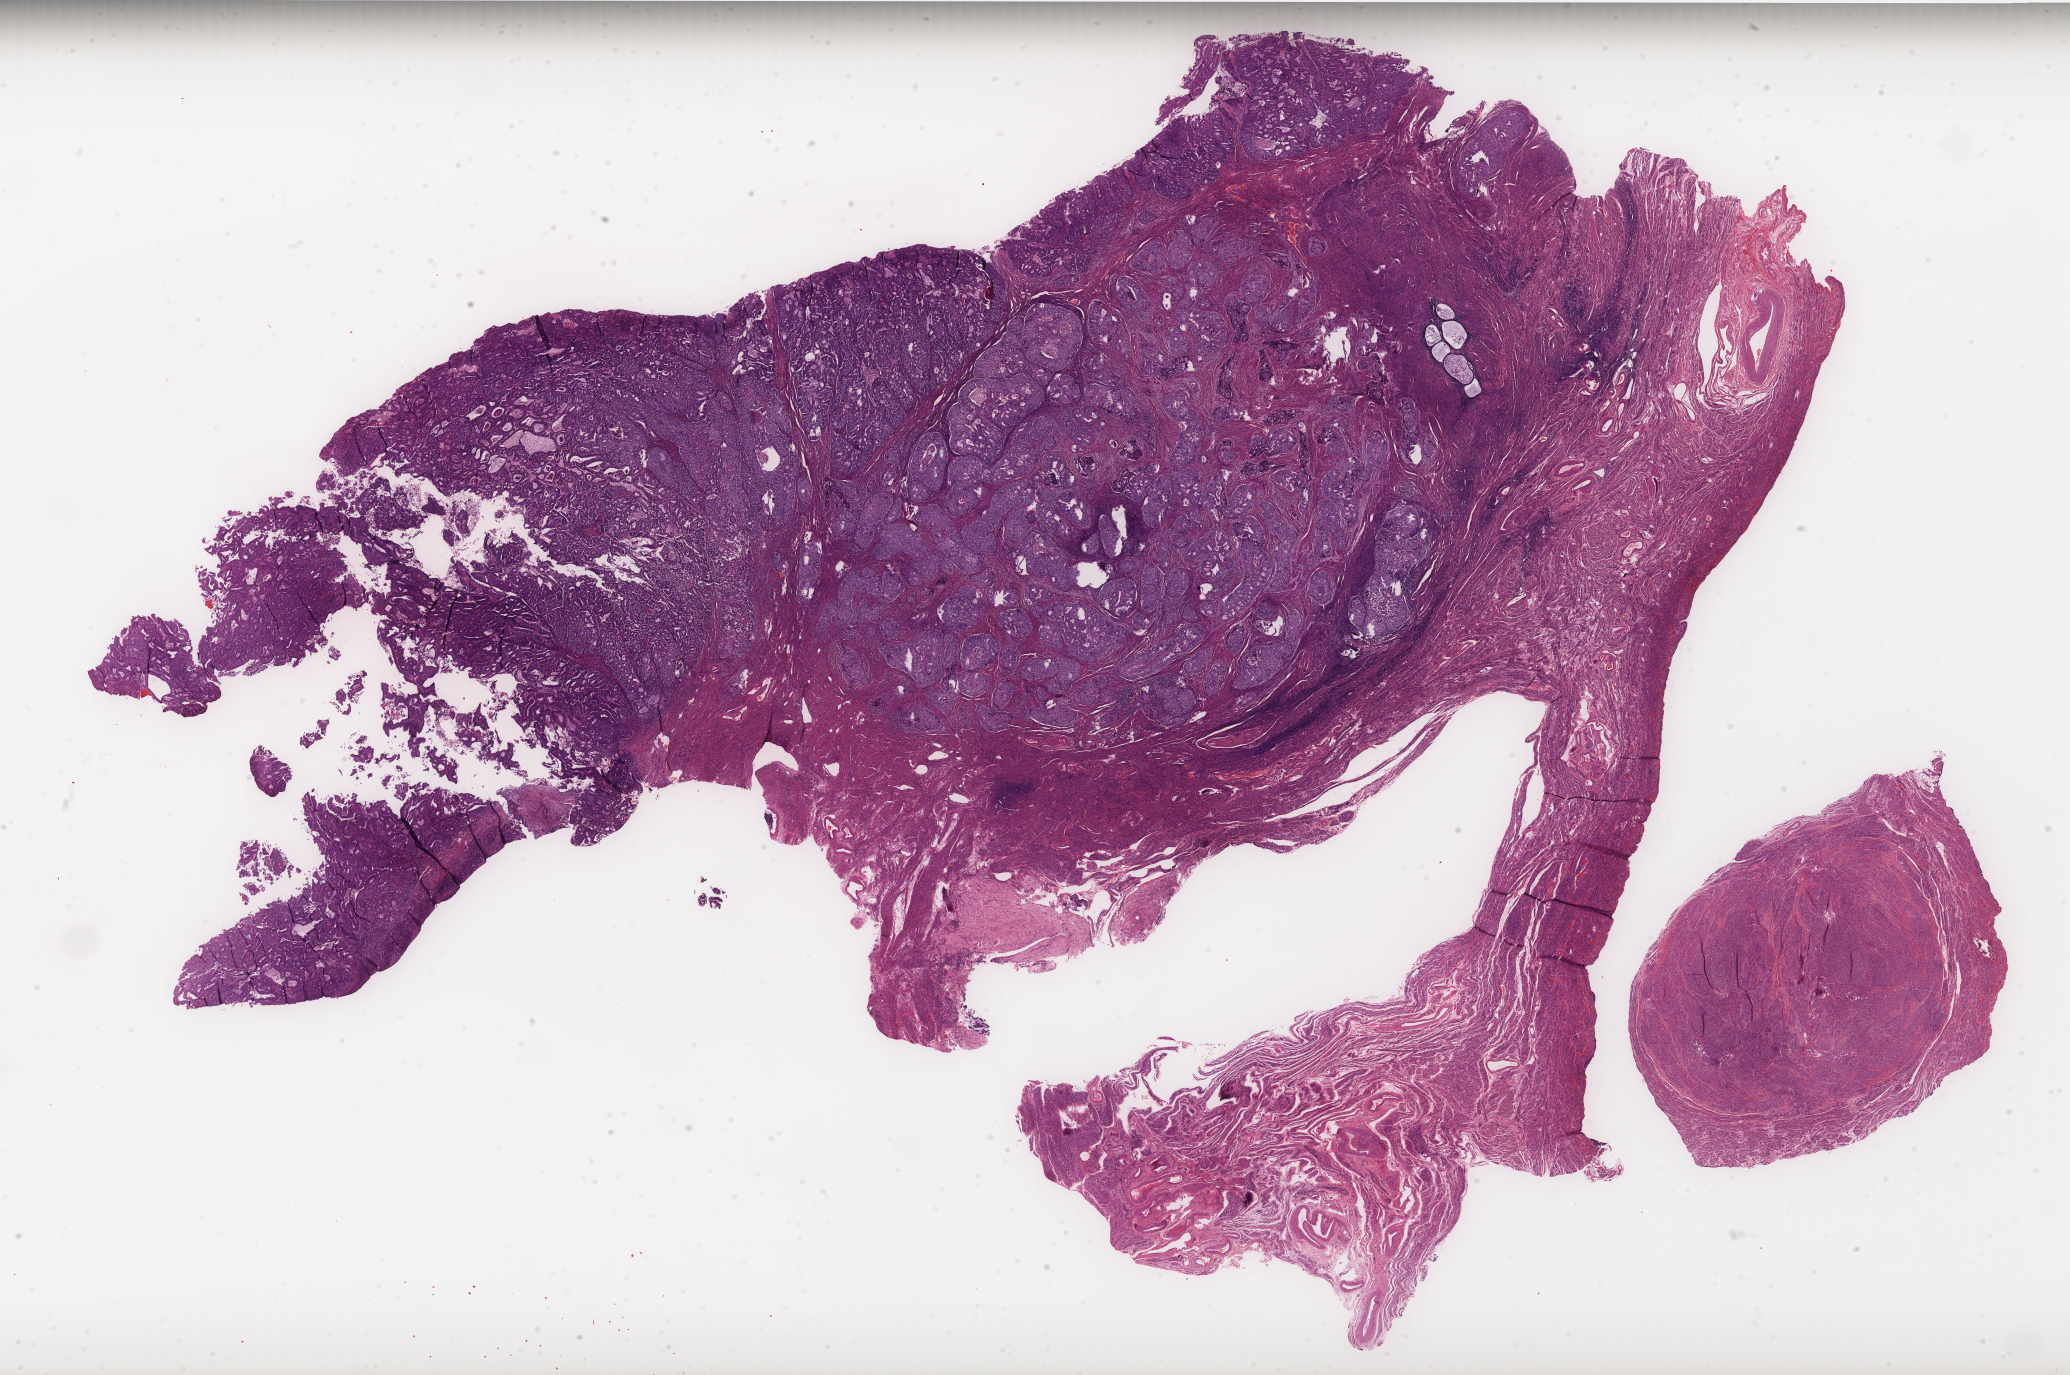
H&E-stained whole-slide image — low-resolution overview of the scanned area, about 33.2 x 22.0 mm (slide scanned at 40x), FFPE section, primary tumour sample from the uterus. Female, age 79 years at initial diagnosis.
Pathologic diagnosis: Endometrioid adenocarcinoma, NOS (endometrium).